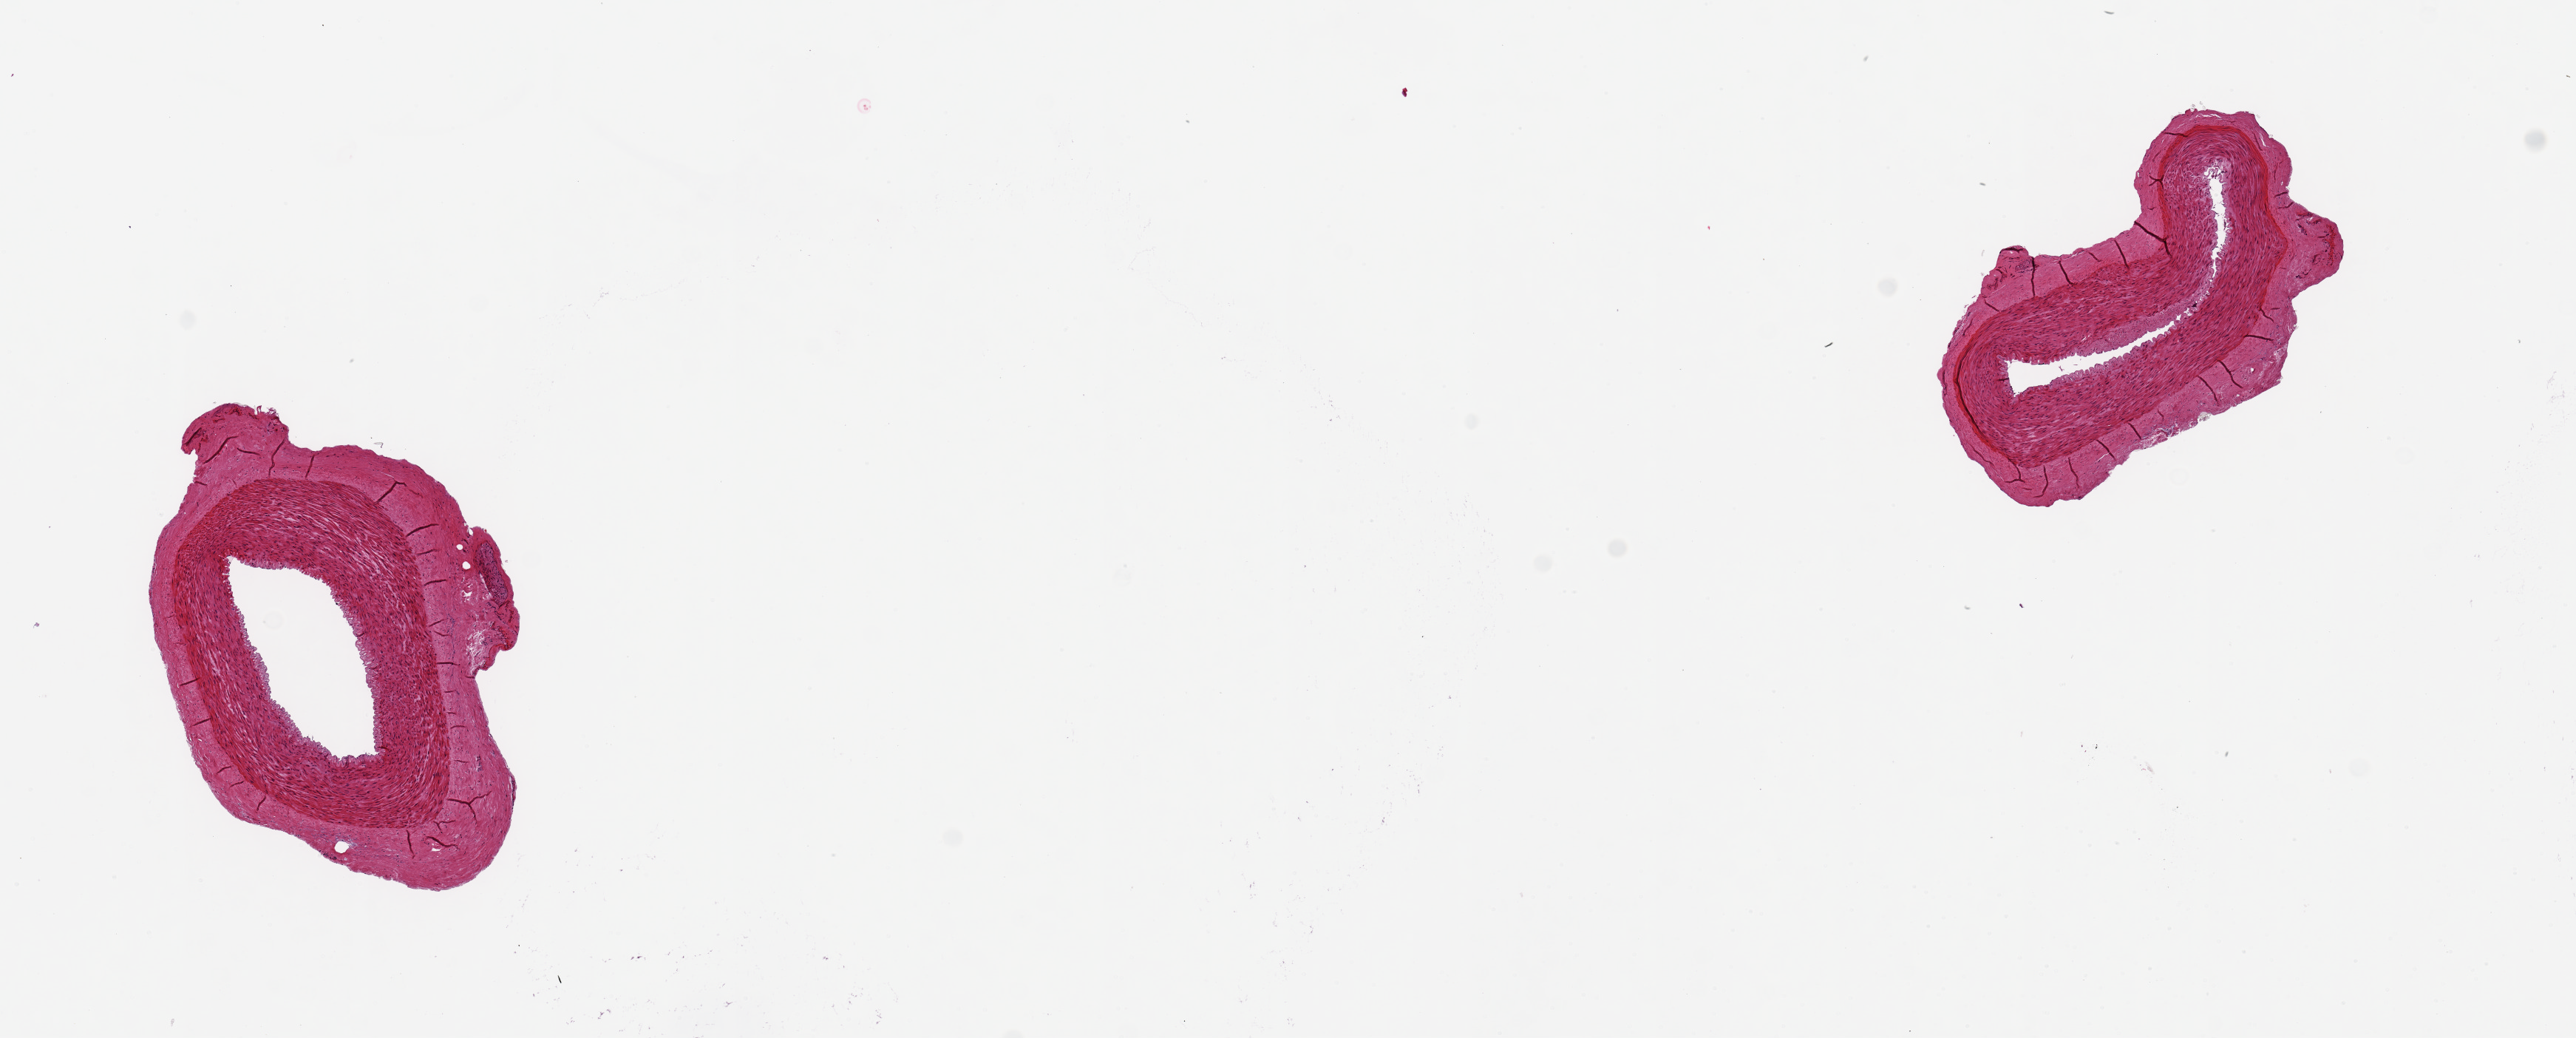
H&E whole-slide image — whole scanned area (about 13.8 x 5.6 mm, from a 20x scan) shown as a low-resolution overview; PAXgene-fixed paraffin-embedded (PFPE) section; section of tibial artery (target tissue); tissue donor sample. Male donor.
Pathologist's review note for this sample: 2 pieces ~2mm d. Good clean specimens.